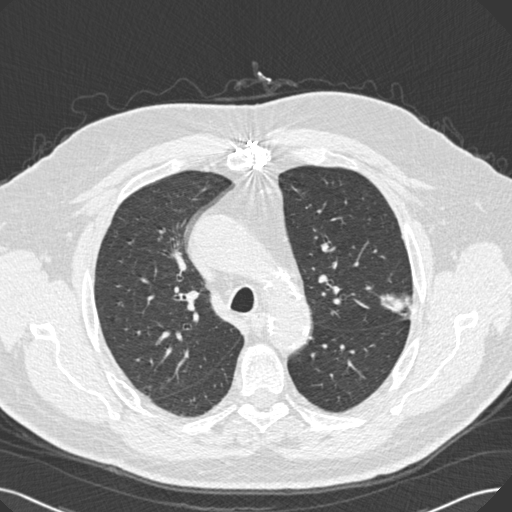
Low-dose screening chest CT, one axial slice. Slice 184 of 269 in the series (ordered by position). Reconstruction kernel B30f. 120 kVp. Lung window (W 1500 / L -600 HU). 1 mm slice thickness. 512 × 512 image matrix, field of view 370 × 370 mm.
Annotated regions visible in this slice (manually delineated by an expert):
- lesion 1 (tumor, upper lobe of left lung): box from (x=380, y=294) to (x=411, y=319) px